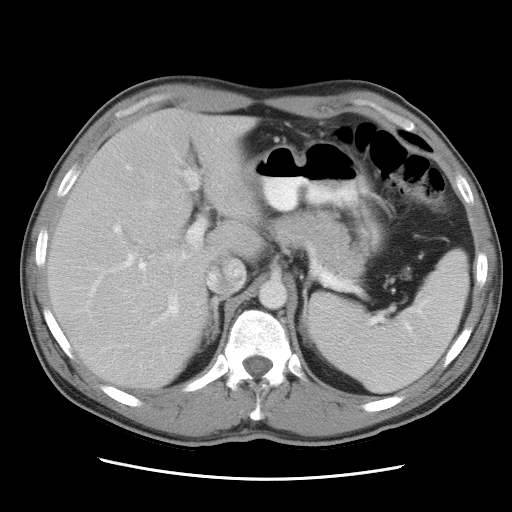
Contrast-enhanced abdominal CT, one axial slice. Position 20 of 34 along the scan axis. Reconstruction kernel STANDARD. 120 kVp. Intravenous contrast given. Soft-tissue window (W 400 / L 40 HU). 7.5 mm slice thickness. 512 × 512 image matrix, field of view 360 × 360 mm. Male patient, age 40 years. From the clinical record (not read from this slice): diagnosis: colorectal cancer liver metastases, imaged before liver resection; multiple liver metastases: yes; largest metastasis: 1.5 cm; chemotherapy before resection: no.
Outlined on this slice (outlined manually by an expert reader):
- liver: bounding box [x1, y1, x2, y2] px = [49, 109, 264, 387]
- planned liver remnant (the part of the liver to remain after resection): [49, 109, 263, 387]
- portal vein (with intrahepatic branches): [89, 171, 205, 323]